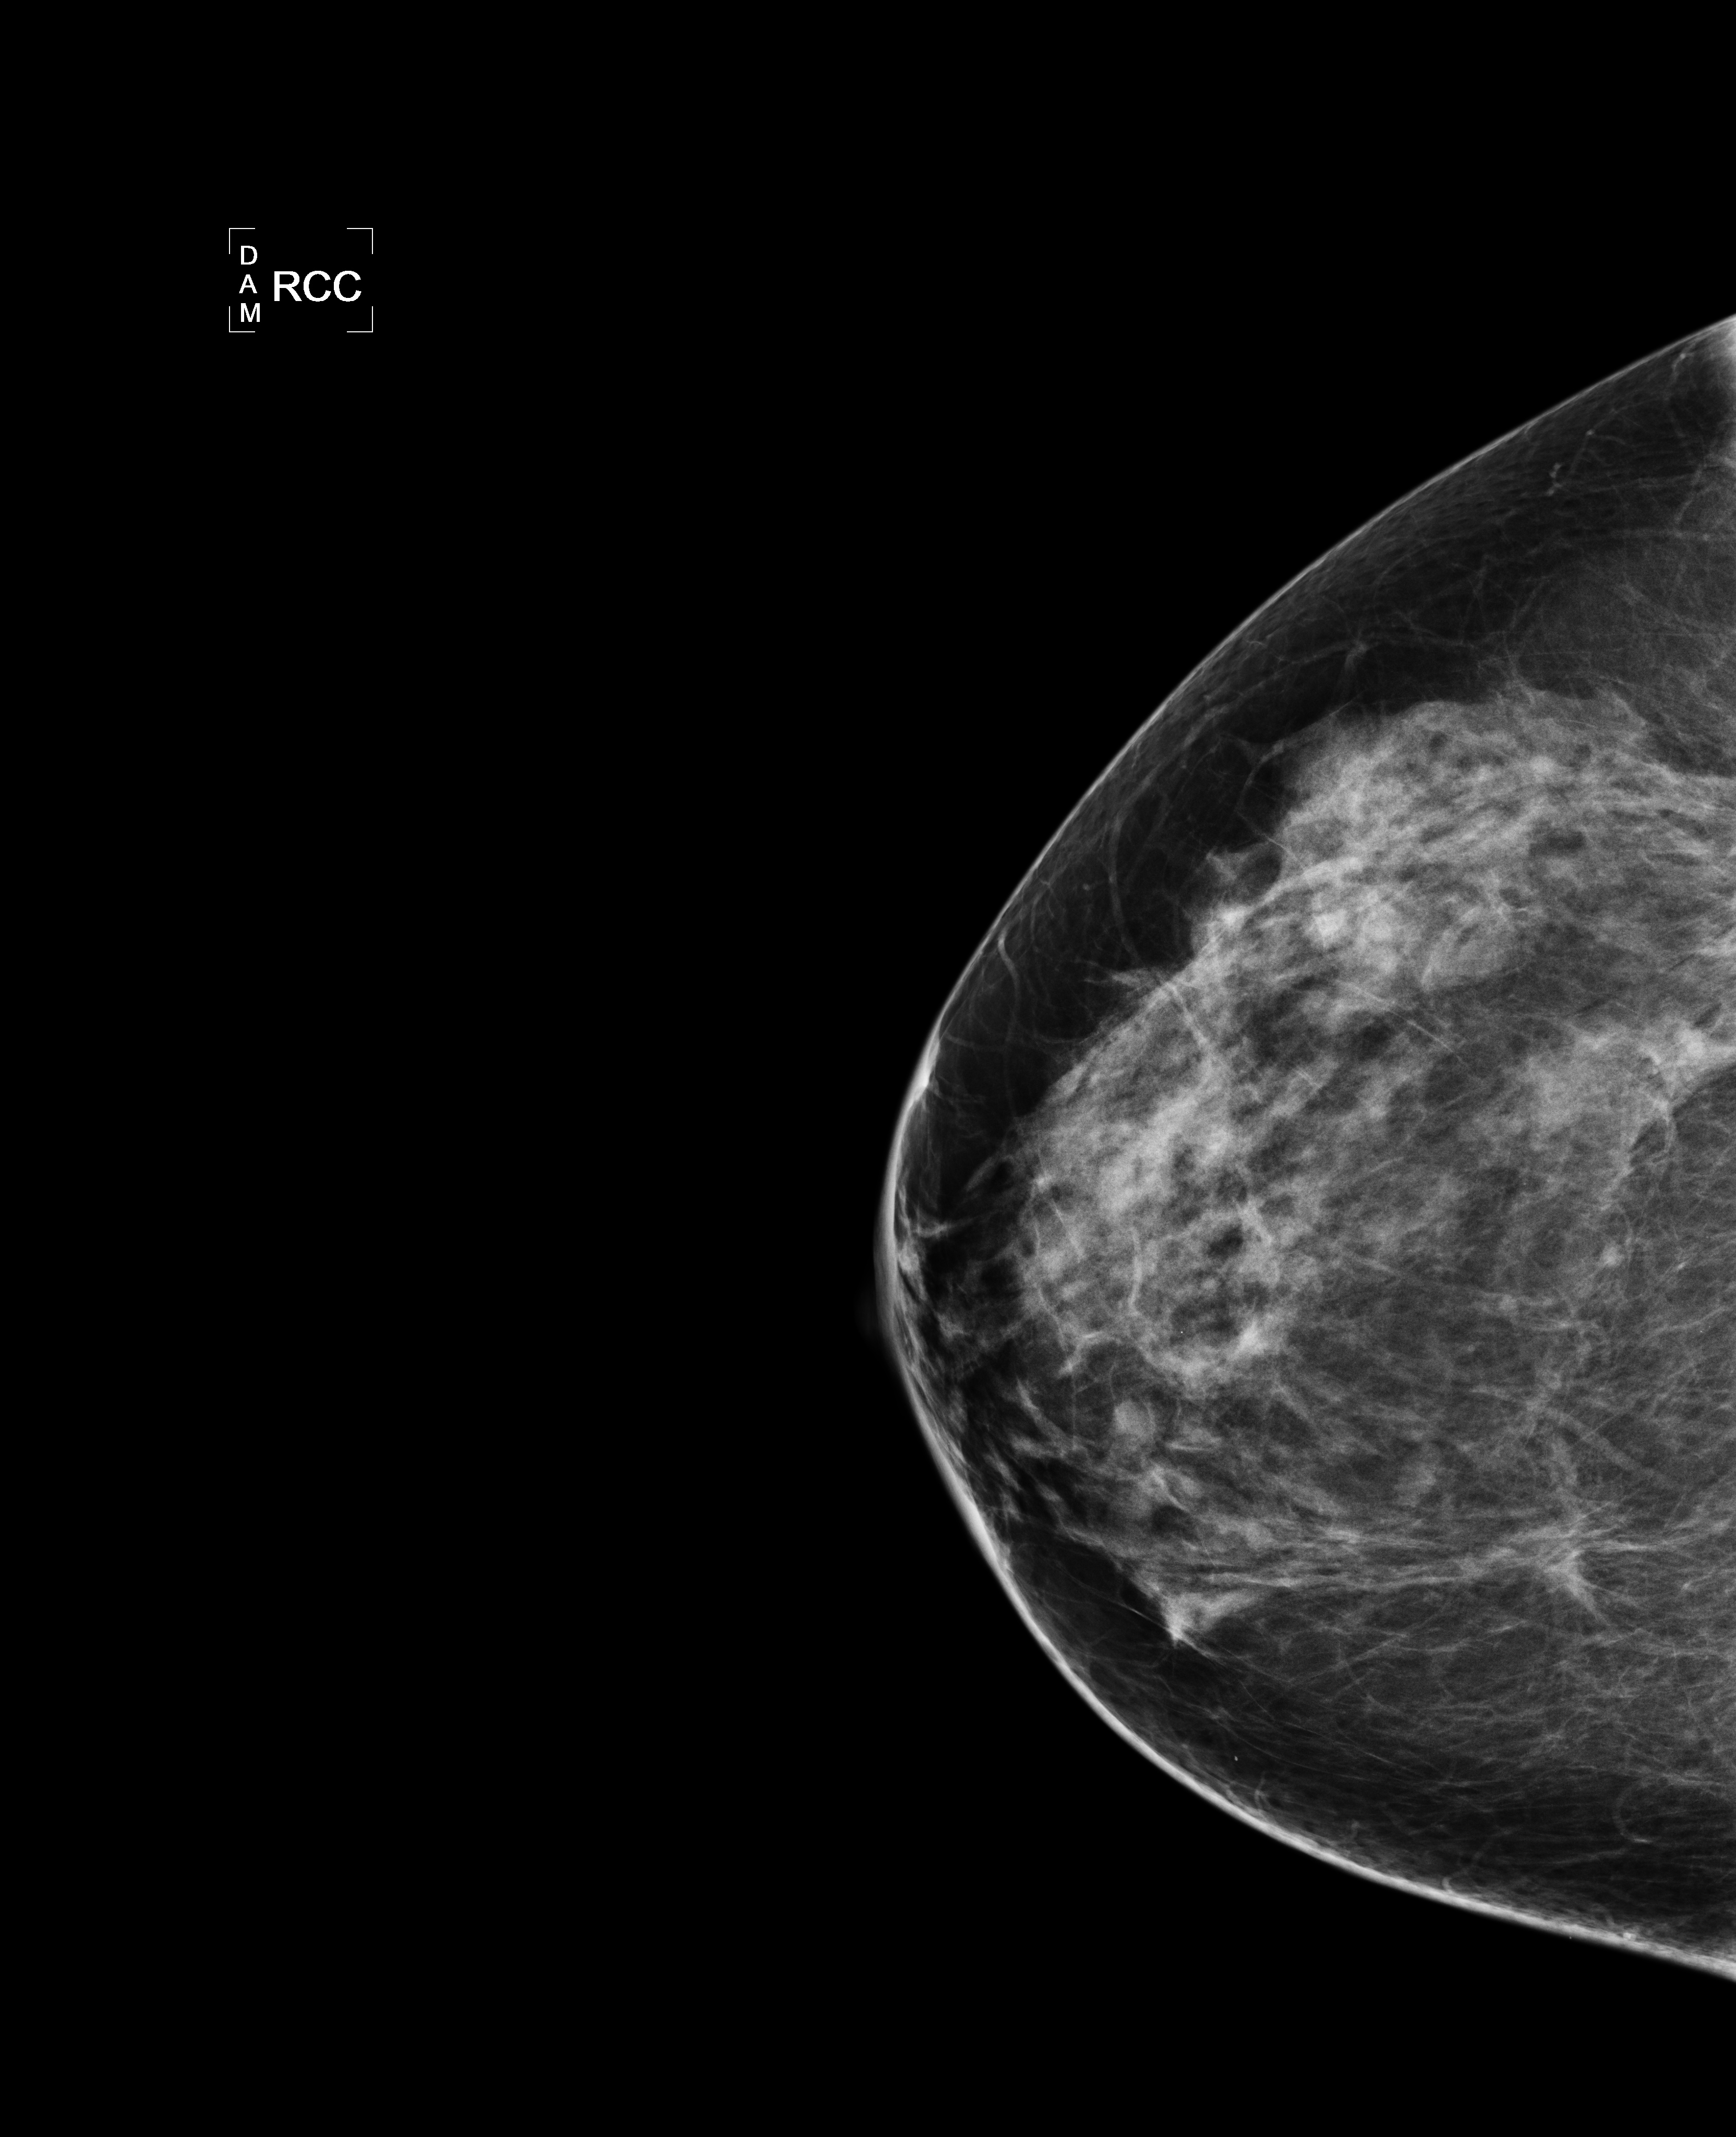
Mammogram, right breast, CC view; patient in her 50s.
Patient-level pathology facts (clinical record, not image findings): pathology diagnosis: Invasive ductal CA (left breast); receptor status (as recorded): ER pos, PR pos (weak), HER2 neg; pathology report notes: re-bx [date] was scar tissue from RT rx.